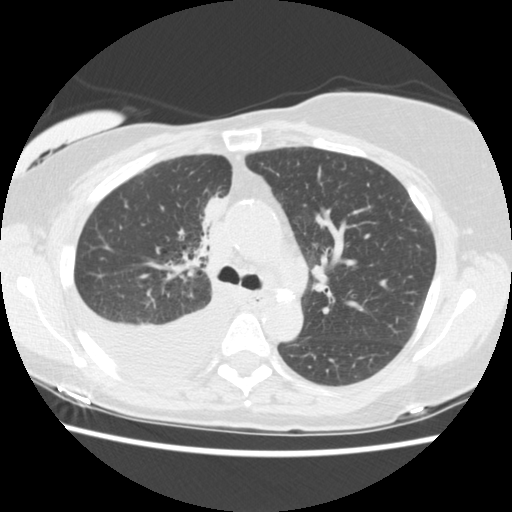
Low-dose screening chest CT, one axial slice. Position 100 of 157 along the scan axis. Reconstruction kernel STANDARD. 120 kVp. Lung window (W 1500 / L -600 HU). 512 × 512 image matrix.
Outlined on this slice (outlined manually by an expert reader):
- lesion 1 (tumor, upper lobe of right lung): bounding box (x1, y1, x2, y2) in pixels: (202, 197, 227, 225)